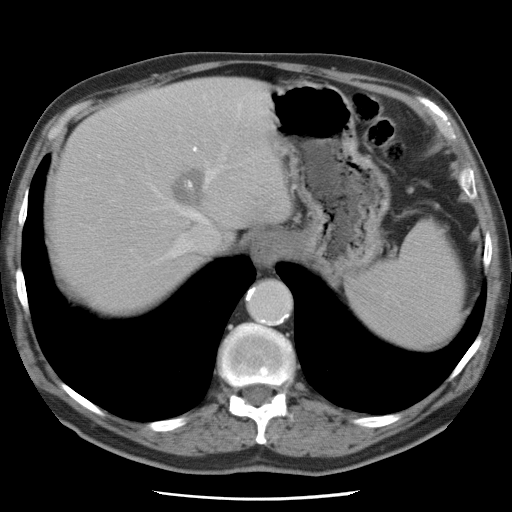
Contrast-enhanced abdominal CT, one axial slice. Position 63 of 78 along the scan axis. 120 kVp. Intravenous contrast given. Soft-tissue window (W 400 / L 40 HU). 5 mm slice thickness. 512 × 512 image matrix, field of view 337 × 337 mm. Male patient, age 75 years. From the clinical record (not read from this slice): diagnosis: colorectal cancer liver metastases, imaged before liver resection; multiple liver metastases: yes.
Annotated regions visible in this slice (manually delineated by an expert):
- hepatic veins: box from (x=148, y=101) to (x=265, y=258) px
- liver: (x=52, y=79)–(x=290, y=311)
- planned liver remnant (the part of the liver to remain after resection): (x=53, y=136)–(x=199, y=313)
- liver metastasis: (x=171, y=169)–(x=206, y=207)